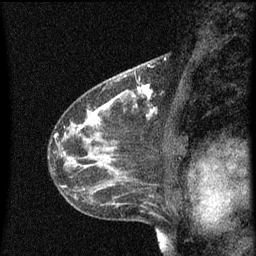
Breast MRI (dynamic contrast-enhanced), one sagittal slice; position 33 of 60 along the scan axis; dynamic contrast-enhanced series, image 2 of 3 at this slice position (ordered by acquisition); 1.5 T; TE 4.2 ms, TR 8 ms; 2 mm slice thickness; 256 × 256 image matrix. Female patient, age 41 years.
Annotated regions visible in this slice (semi-automatically segmented with operator editing):
- analysis volume of interest (the breast-tissue region the enhancement analysis was run in; not a lesion): bounding box [x1, y1, x2, y2] px = [130, 76, 153, 103]
- tumour enhancement mask (voxels above the 70 % enhancement threshold inside the analysis volume of interest): [132, 78, 153, 99]